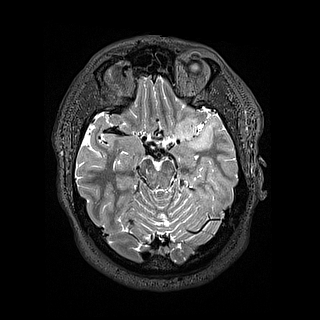
Brain MRI from a brain-tumour surgery series, one axial slice; slice 100 of 144 in the series (ordered by position); 1.2 mm slice thickness; 320 × 320 image matrix, field of view 254 × 254 mm. Case-level facts recorded for this patient, not image findings: histopathology: Astrocytoma; WHO grade: 2; IDH mutation: yes.
Annotated regions visible in this slice (manually delineated by an expert):
- tumour: box from (x=173, y=113) to (x=205, y=152) px